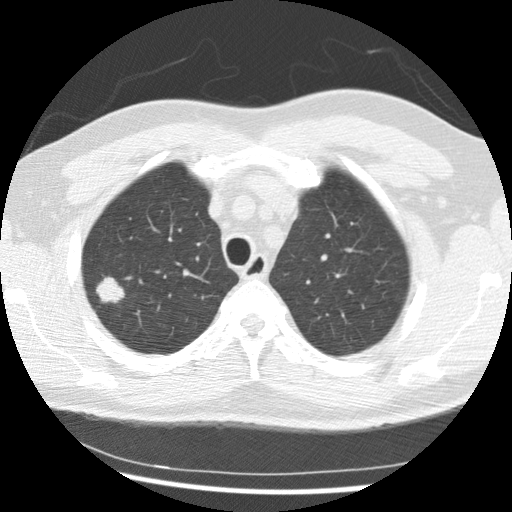
Chest CT (low-dose screening protocol), one axial image. Baseline annual screen. Lung window (W 1500 / L -600 HU). 2.5 mm slice thickness. Male, age 56 years at enrolment. Current smoker at enrolment.
Expert reader's lesion annotation, bounding box <80,271,131,316> (left, top, right, bottom; pixels). Screening reader's record for this exam (one nodule recorded; not confirmed to be the boxed lesion): non-calcified nodule or mass ≥4 mm, right upper lobe, 19 × 15 mm, spiculated (stellate) margins, soft tissue attenuation. Official screen result: positive, change unspecified: nodule(s) >= 4 mm or enlarging nodule(s), mass(es), or other non-specific abnormalities suspicious for lung cancer.